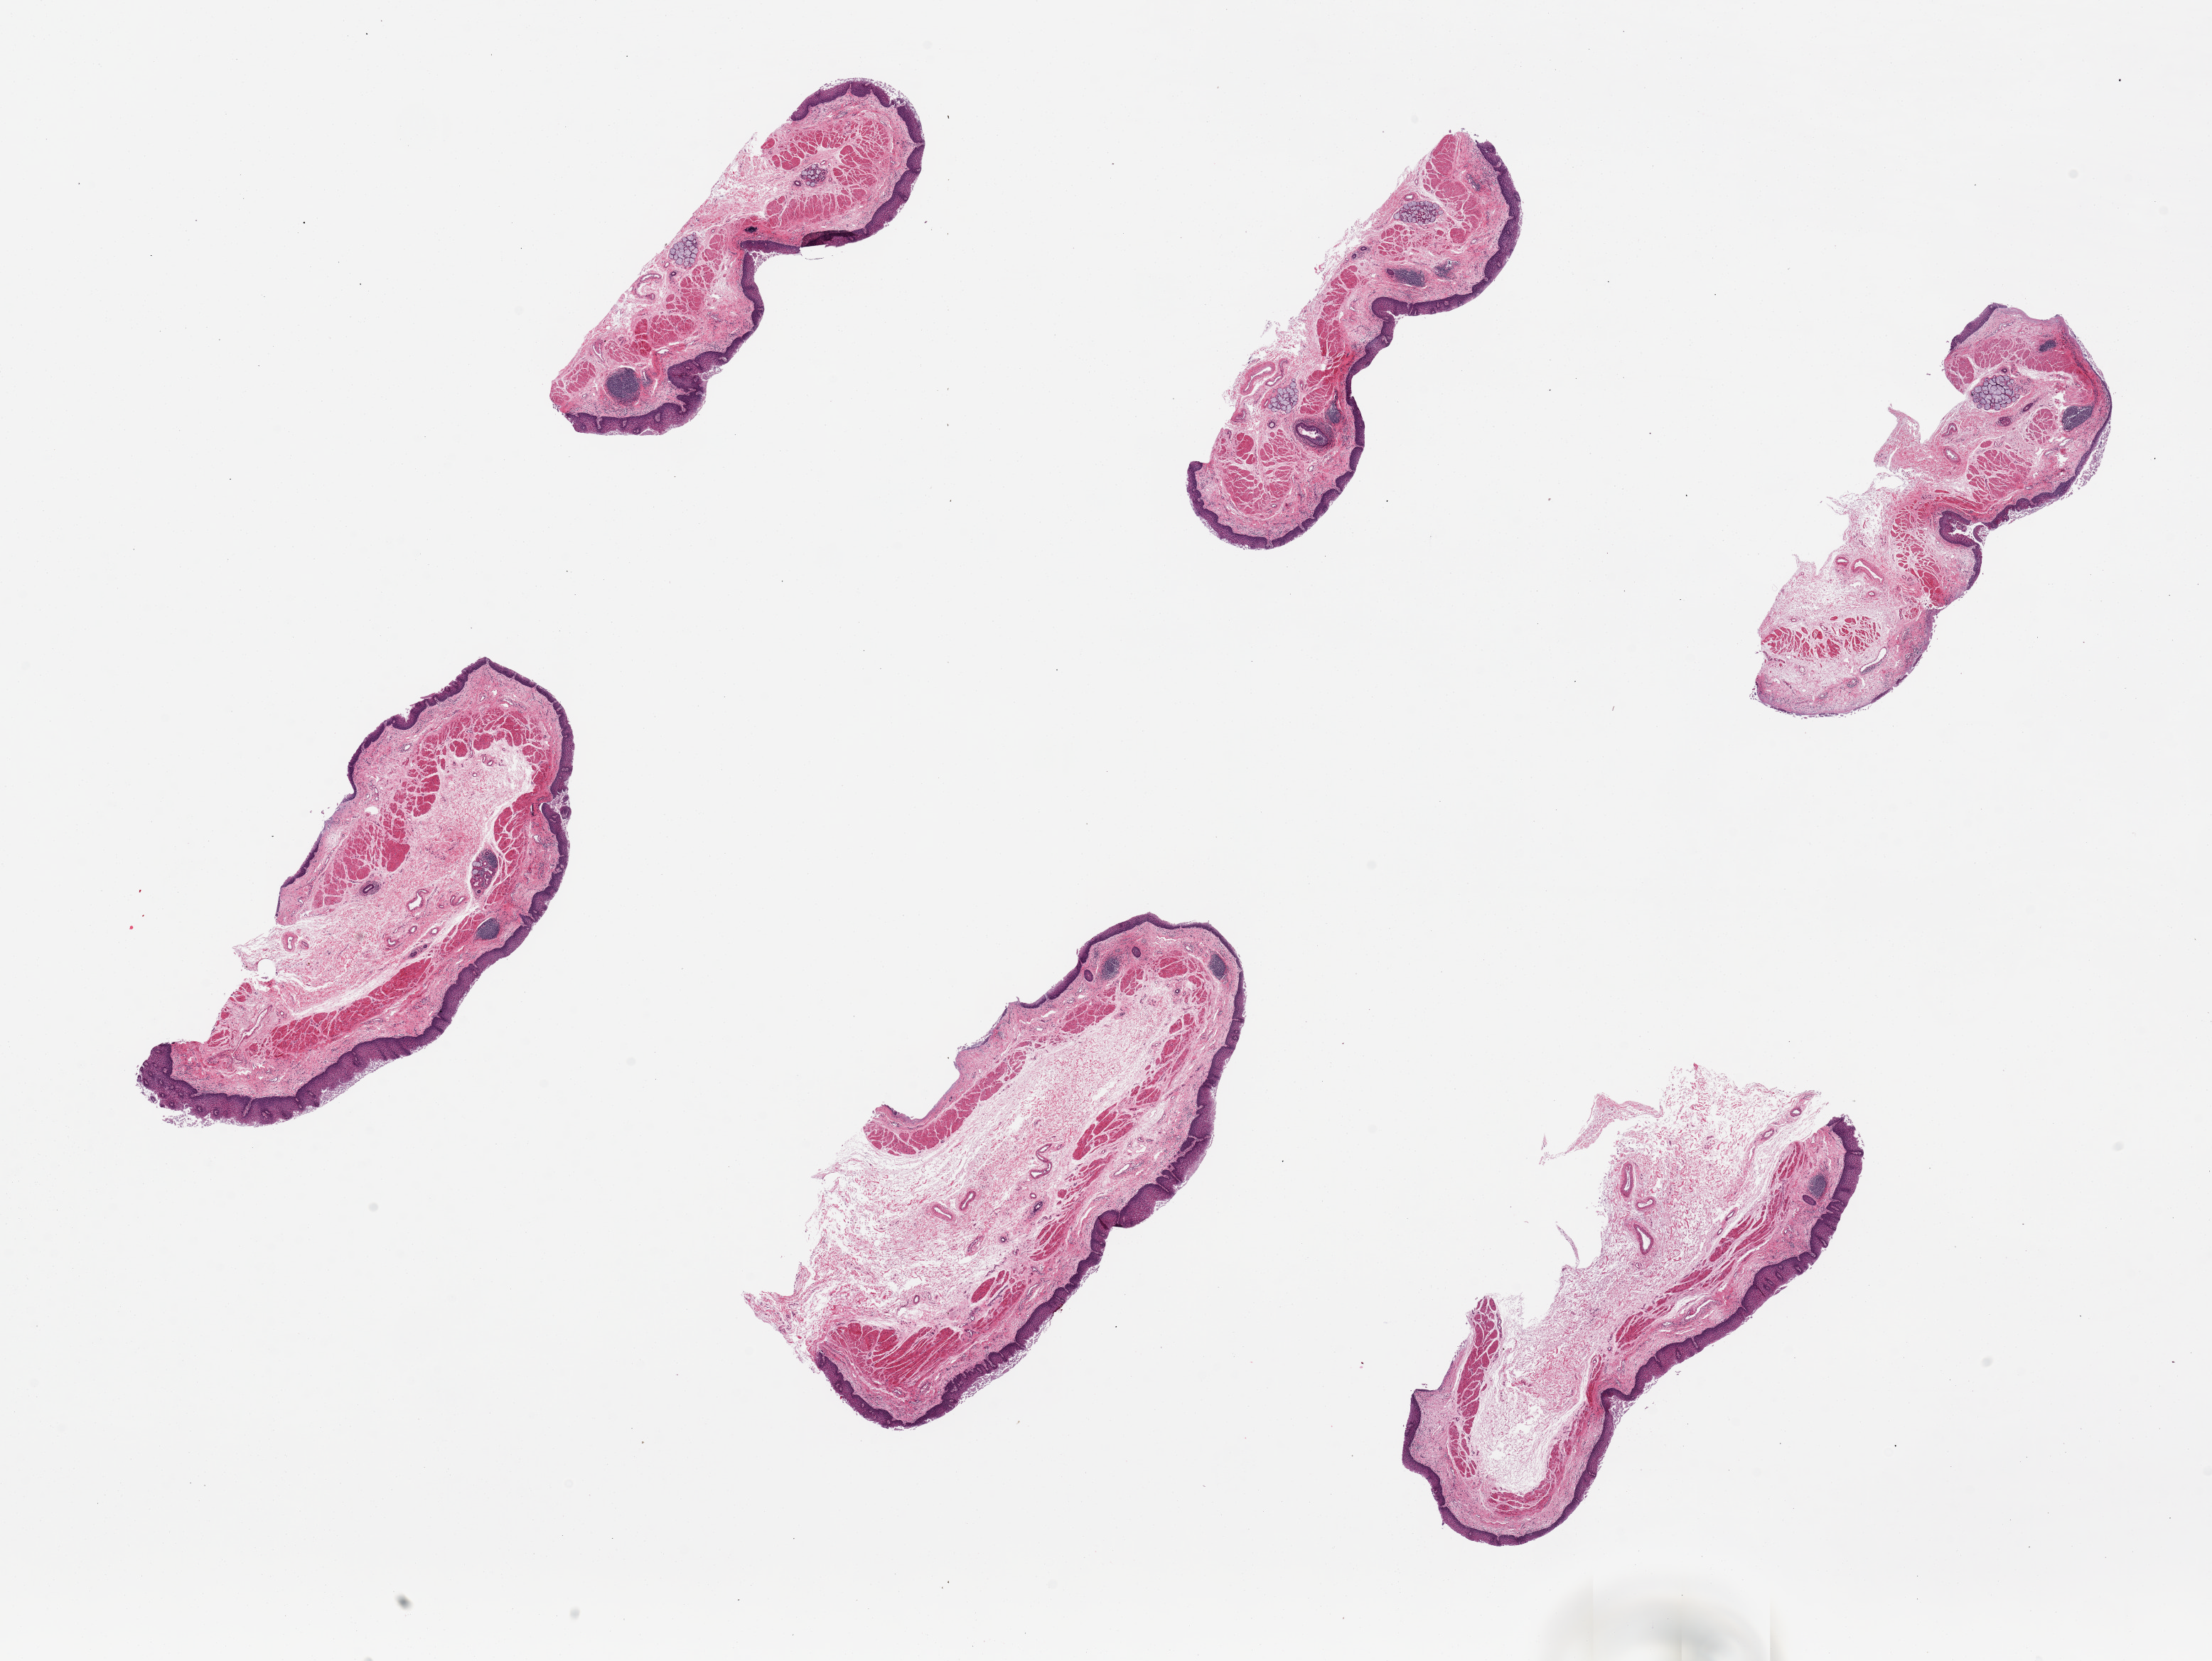
Digitized H&E-stained section, brightfield, whole scanned area (about 24.6 x 18.5 mm, slide scanned at 20x) shown as a low-resolution overview, PAXgene-fixed paraffin-embedded (PFPE) section, sampled site (target tissue): esophageal mucous membrane, tissue donor sample. Donor: female.
- reviewer comment on this tissue sample: 6 pieces, up to 7x3mm; well dissected; surface sloughing, severe in 1 piece